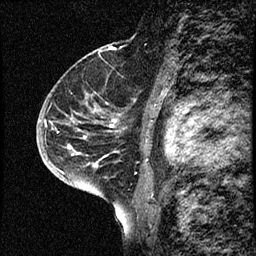
Breast MRI (dynamic contrast-enhanced), one sagittal slice. Position 47 of 68 along the scan axis. Dynamic contrast-enhanced study with each time point stored as its own series, time point 2 of 3 at this slice position (early post-contrast, ordered by acquisition time). 1.5 T. TE 4.2 ms, TR 17.6 ms. 256 × 256 image matrix. Female patient, age 52 years. From the clinical record (not read from this slice): setting: breast cancer imaged before/during neoadjuvant chemotherapy; receptor status: HER2-positive.
Structures marked on this image (semi-automatically segmented with operator editing):
- analysis volume of interest (the breast-tissue region the enhancement analysis was run in; not a lesion): bounding box [x1, y1, x2, y2] px = [50, 61, 139, 184]
- tumour enhancement mask (voxels above the 100 % enhancement threshold inside the analysis volume of interest): [93, 110, 97, 167]